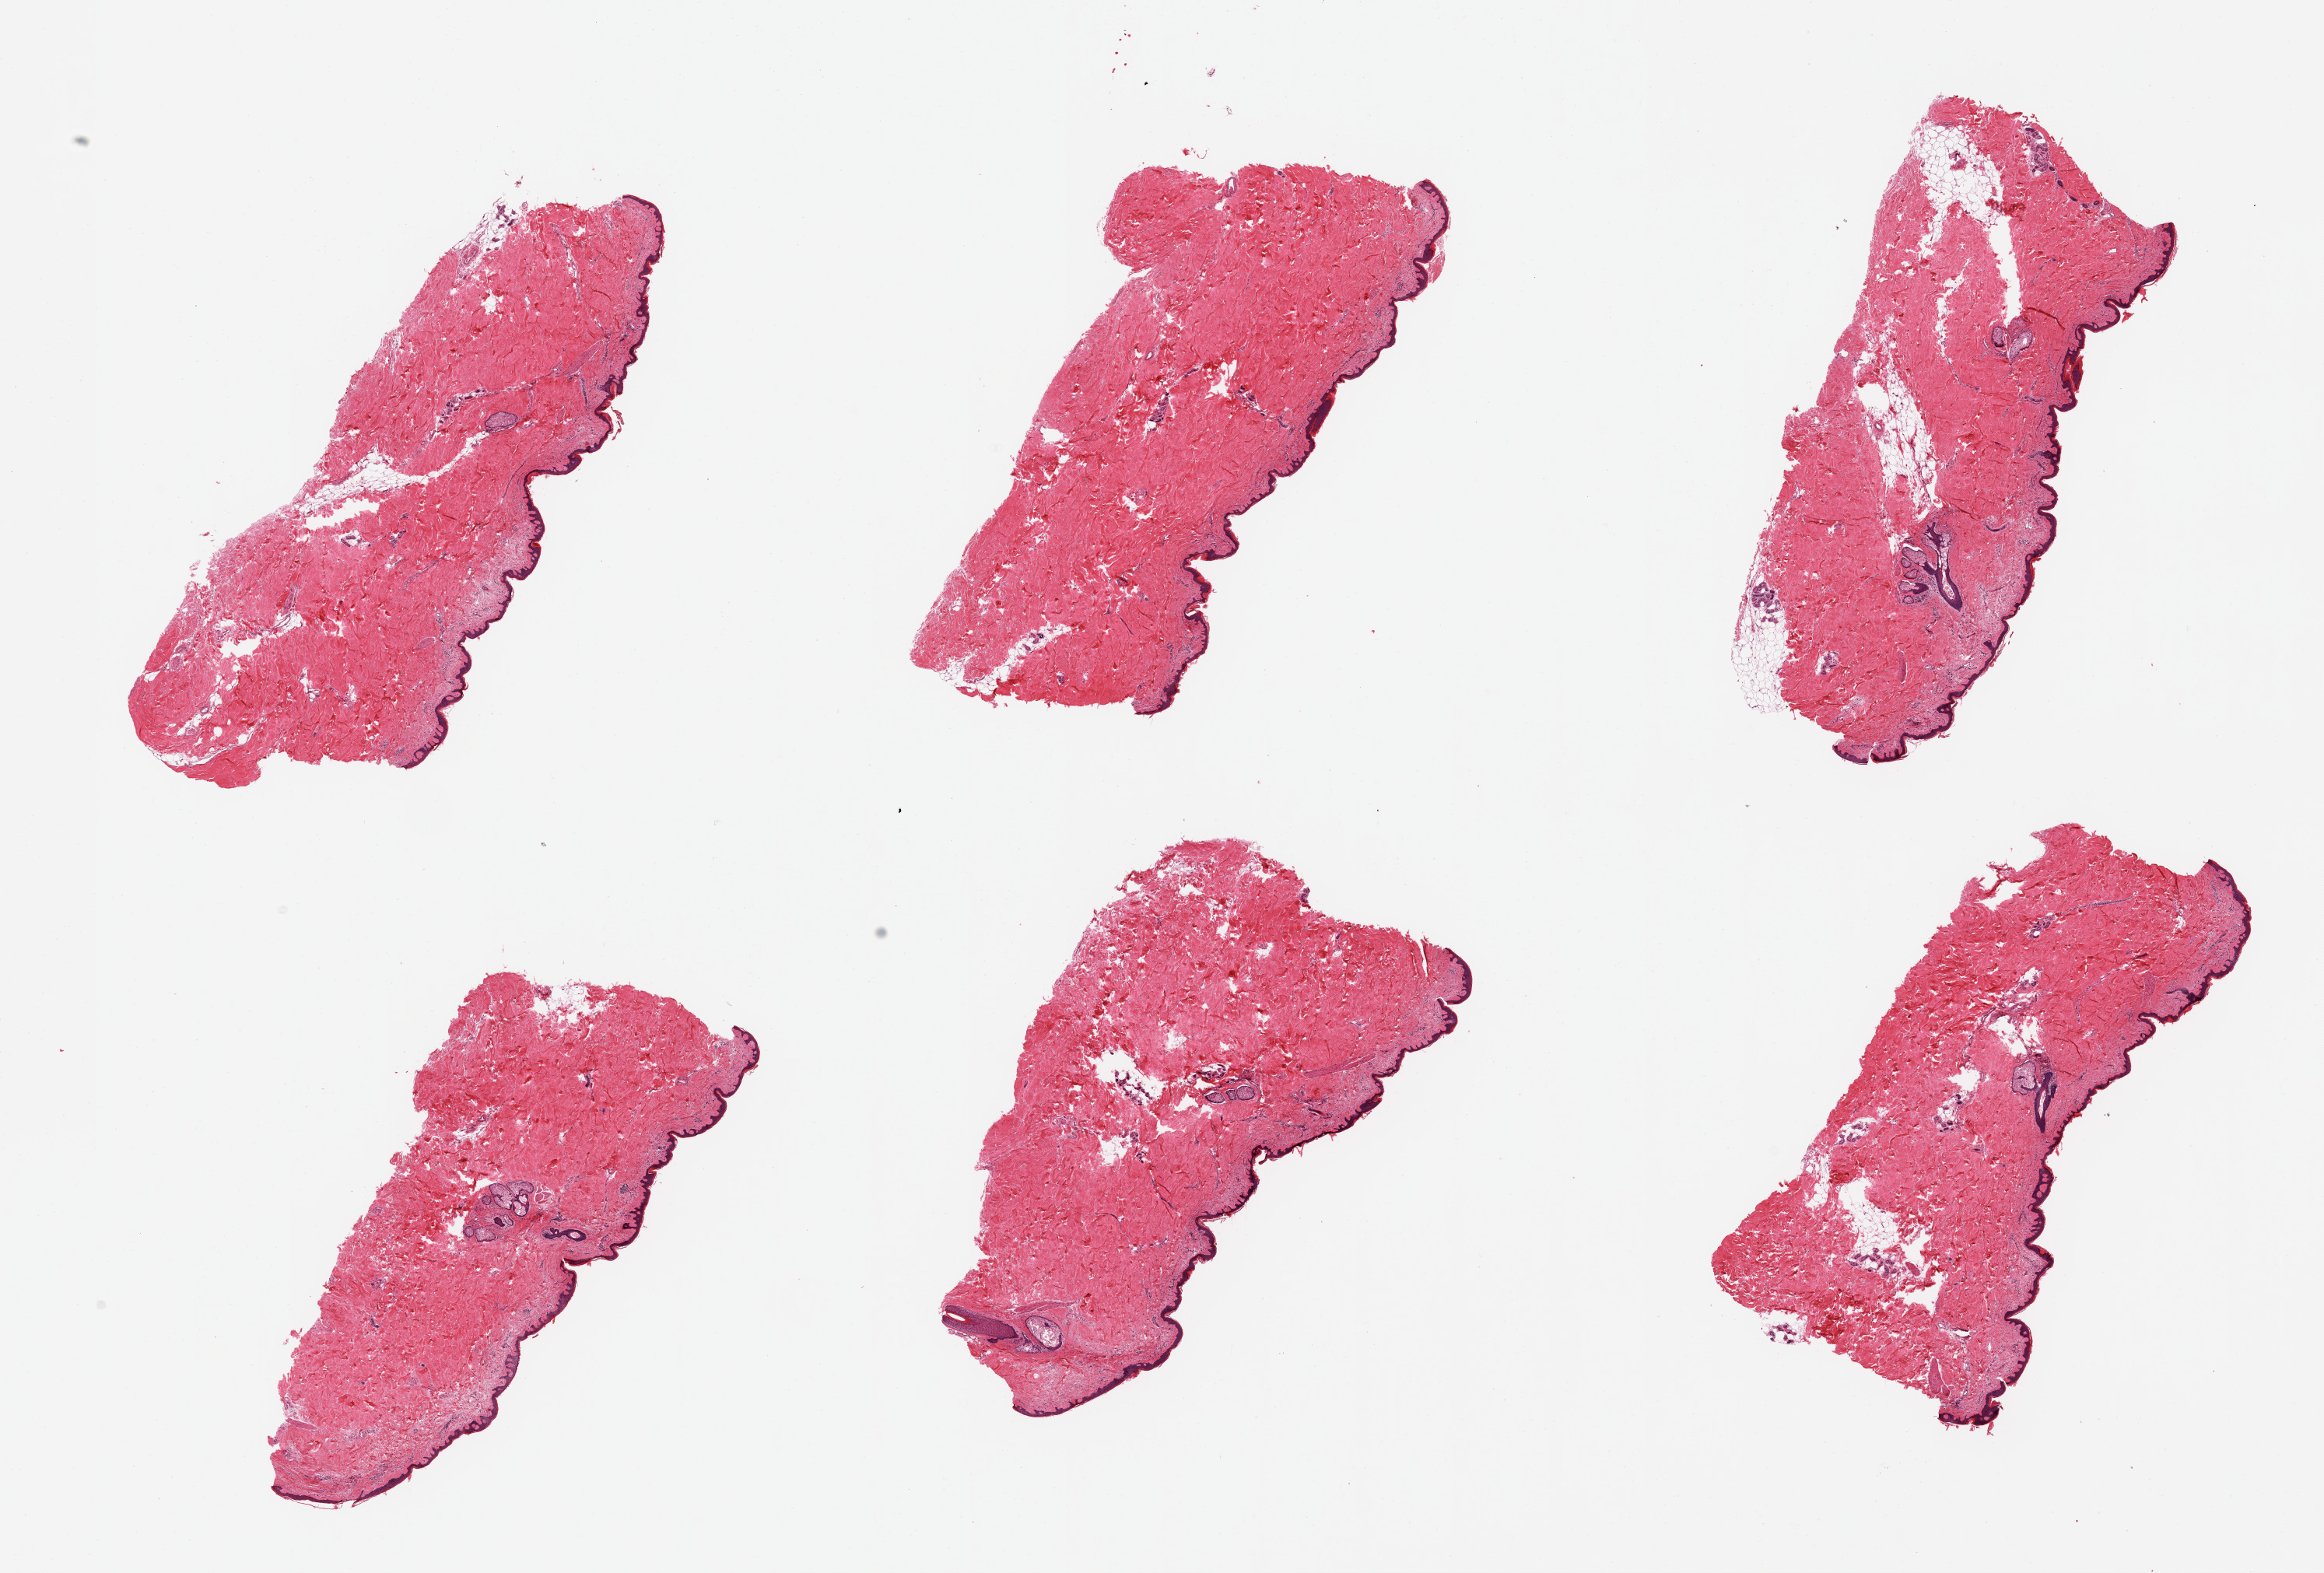
Whole-slide image, H&E stain, brightfield, whole scanned area (about 23.6 x 16.0 mm) shown as a low-resolution overview. PAXgene-fixed, paraffin-embedded tissue. Sampled site (target tissue): skin of lower leg. Tissue donor sample. Male donor.
• review note (as recorded): 6 pieces, squamous epithelium is ~30 microns, minimal/no dermal fat